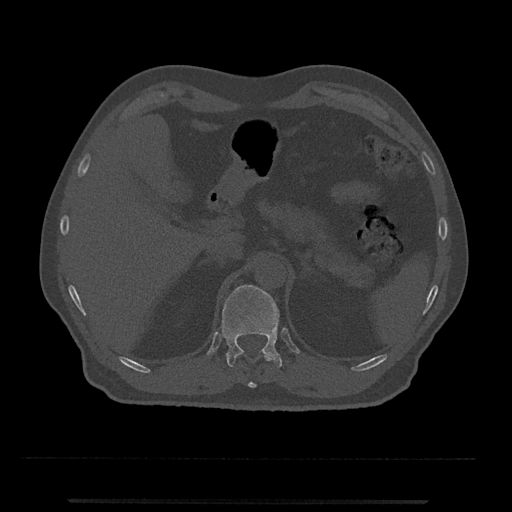
CT including the spine, one axial slice. Position 423 of 797 along the scan axis. Reconstruction kernel Br40s/3. 120 kVp. Bone window (W 1800 / L 400 HU). 512 × 512 image matrix, field of view 419 × 419 mm. Patient: male, 63 years. From the clinical record (not read from this slice): primary cancer: prostate.
Structures marked on this image (semi-automatic segmentation, software-assisted and operator-edited):
- T11 vertebra: bounding box <236,351,272,388> (left, top, right, bottom; pixels)
- T12 vertebra: <222,285,282,367>